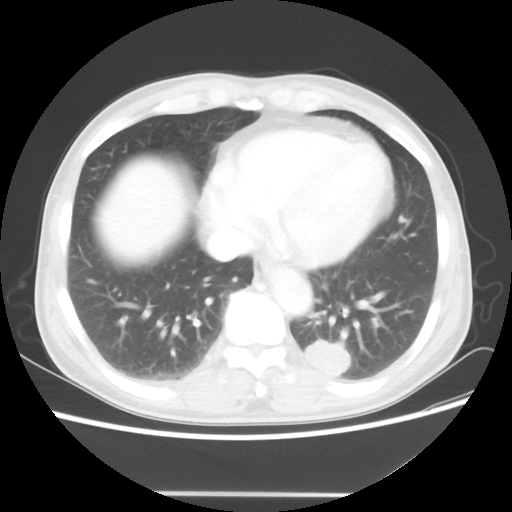
Chest CT, one axial slice; position 19 of 60 along the scan axis; reconstruction kernel STANDARD; 100 kVp; lung window (W 1500 / L -600 HU); 5 mm slice thickness; 512 × 512 image matrix. Male patient, age 55 years. Case-level facts recorded for this patient, not image findings: clinical TNM (as recorded): T1c N3 M0; histopathological grade: G3.
Annotated regions visible in this slice (rectangle marked by the reading radiologist):
- lung tumour (recorded histology: small cell carcinoma): bounding box (x1, y1, x2, y2) in pixels: (301, 341, 354, 386)